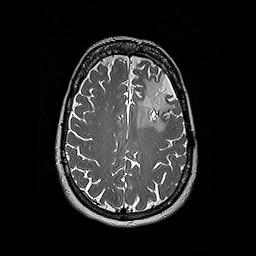
Brain MRI from a brain-tumour surgery series, one axial slice. Slice 128 of 192 in the series (ordered by position). 1 mm slice thickness. 256 × 256 image matrix, field of view 250 × 250 mm. Case-level facts recorded for this patient, not image findings: histopathology: Oligodendroglioma; WHO grade: 2; IDH mutation: yes; tumour location: Left Frontal.
Structures marked on this image (manually delineated by an expert):
- tumour: bounding box <135,79,159,127> (left, top, right, bottom; pixels)